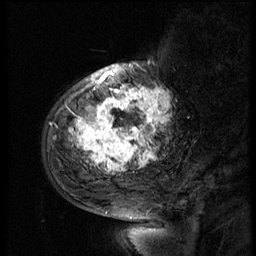
Breast MRI (dynamic contrast-enhanced), one sagittal slice; slice 16 of 56 in the series (ordered by position); 3 images stored at this slice position (order not interpretable as contrast timing); 1.5 T; TE 4.2 ms, TR 9 ms; 2.5 mm slice thickness; 256 × 256 image matrix, field of view 180 × 180 mm. Female patient, age 51 years. Case-level facts recorded for this patient, not image findings: setting: breast cancer imaged before/during neoadjuvant chemotherapy; receptor status: triple-negative.
Annotated regions visible in this slice (semi-automatically segmented with operator editing):
- analysis volume of interest (the breast-tissue region the enhancement analysis was run in; not a lesion): bounding box <52,66,183,179> (left, top, right, bottom; pixels)
- tumour enhancement mask (voxels above the 140 % enhancement threshold inside the analysis volume of interest): <70,72,171,173>